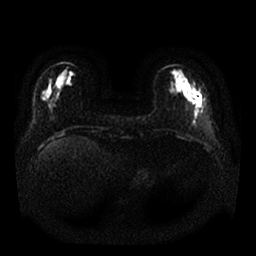
Breast MRI, one axial slice. Diffusion-weighted series; image 2 of 4 stored at this slice position (different b-values; order by instance number). 1.5 T. 4 mm slice thickness. 256 × 256 image matrix, field of view 340 × 340 mm. Female patient.
Annotated regions visible in this slice (outlined manually by an expert reader):
- tumour on diffusion-weighted imaging: bounding box (x1, y1, x2, y2) in pixels: (192, 82, 203, 107)